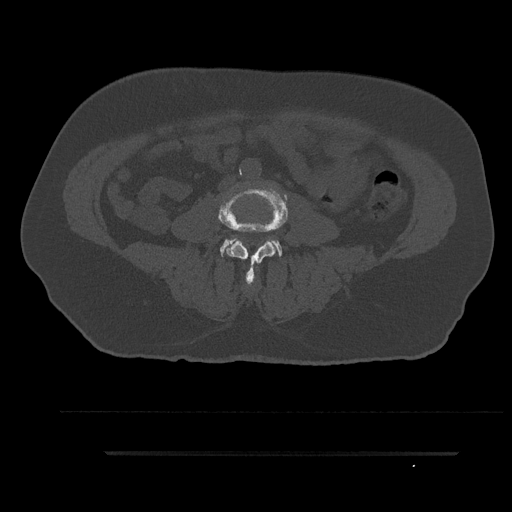
CT including the spine, one axial slice. Slice 14 of 797 in the series (ordered by position). 120 kVp. Bone window (W 1800 / L 400 HU). 0.5 mm slice thickness. 512 × 512 image matrix. Patient: male, 63 years. From the clinical record (not read from this slice): primary cancer: renal; vertebrae with lytic lesions (as recorded): T8.
Outlined on this slice (semi-automatic segmentation, software-assisted and operator-edited):
- L3 vertebra: bounding box <218,186,289,285> (left, top, right, bottom; pixels)
- L4 vertebra: <220,236,283,257>